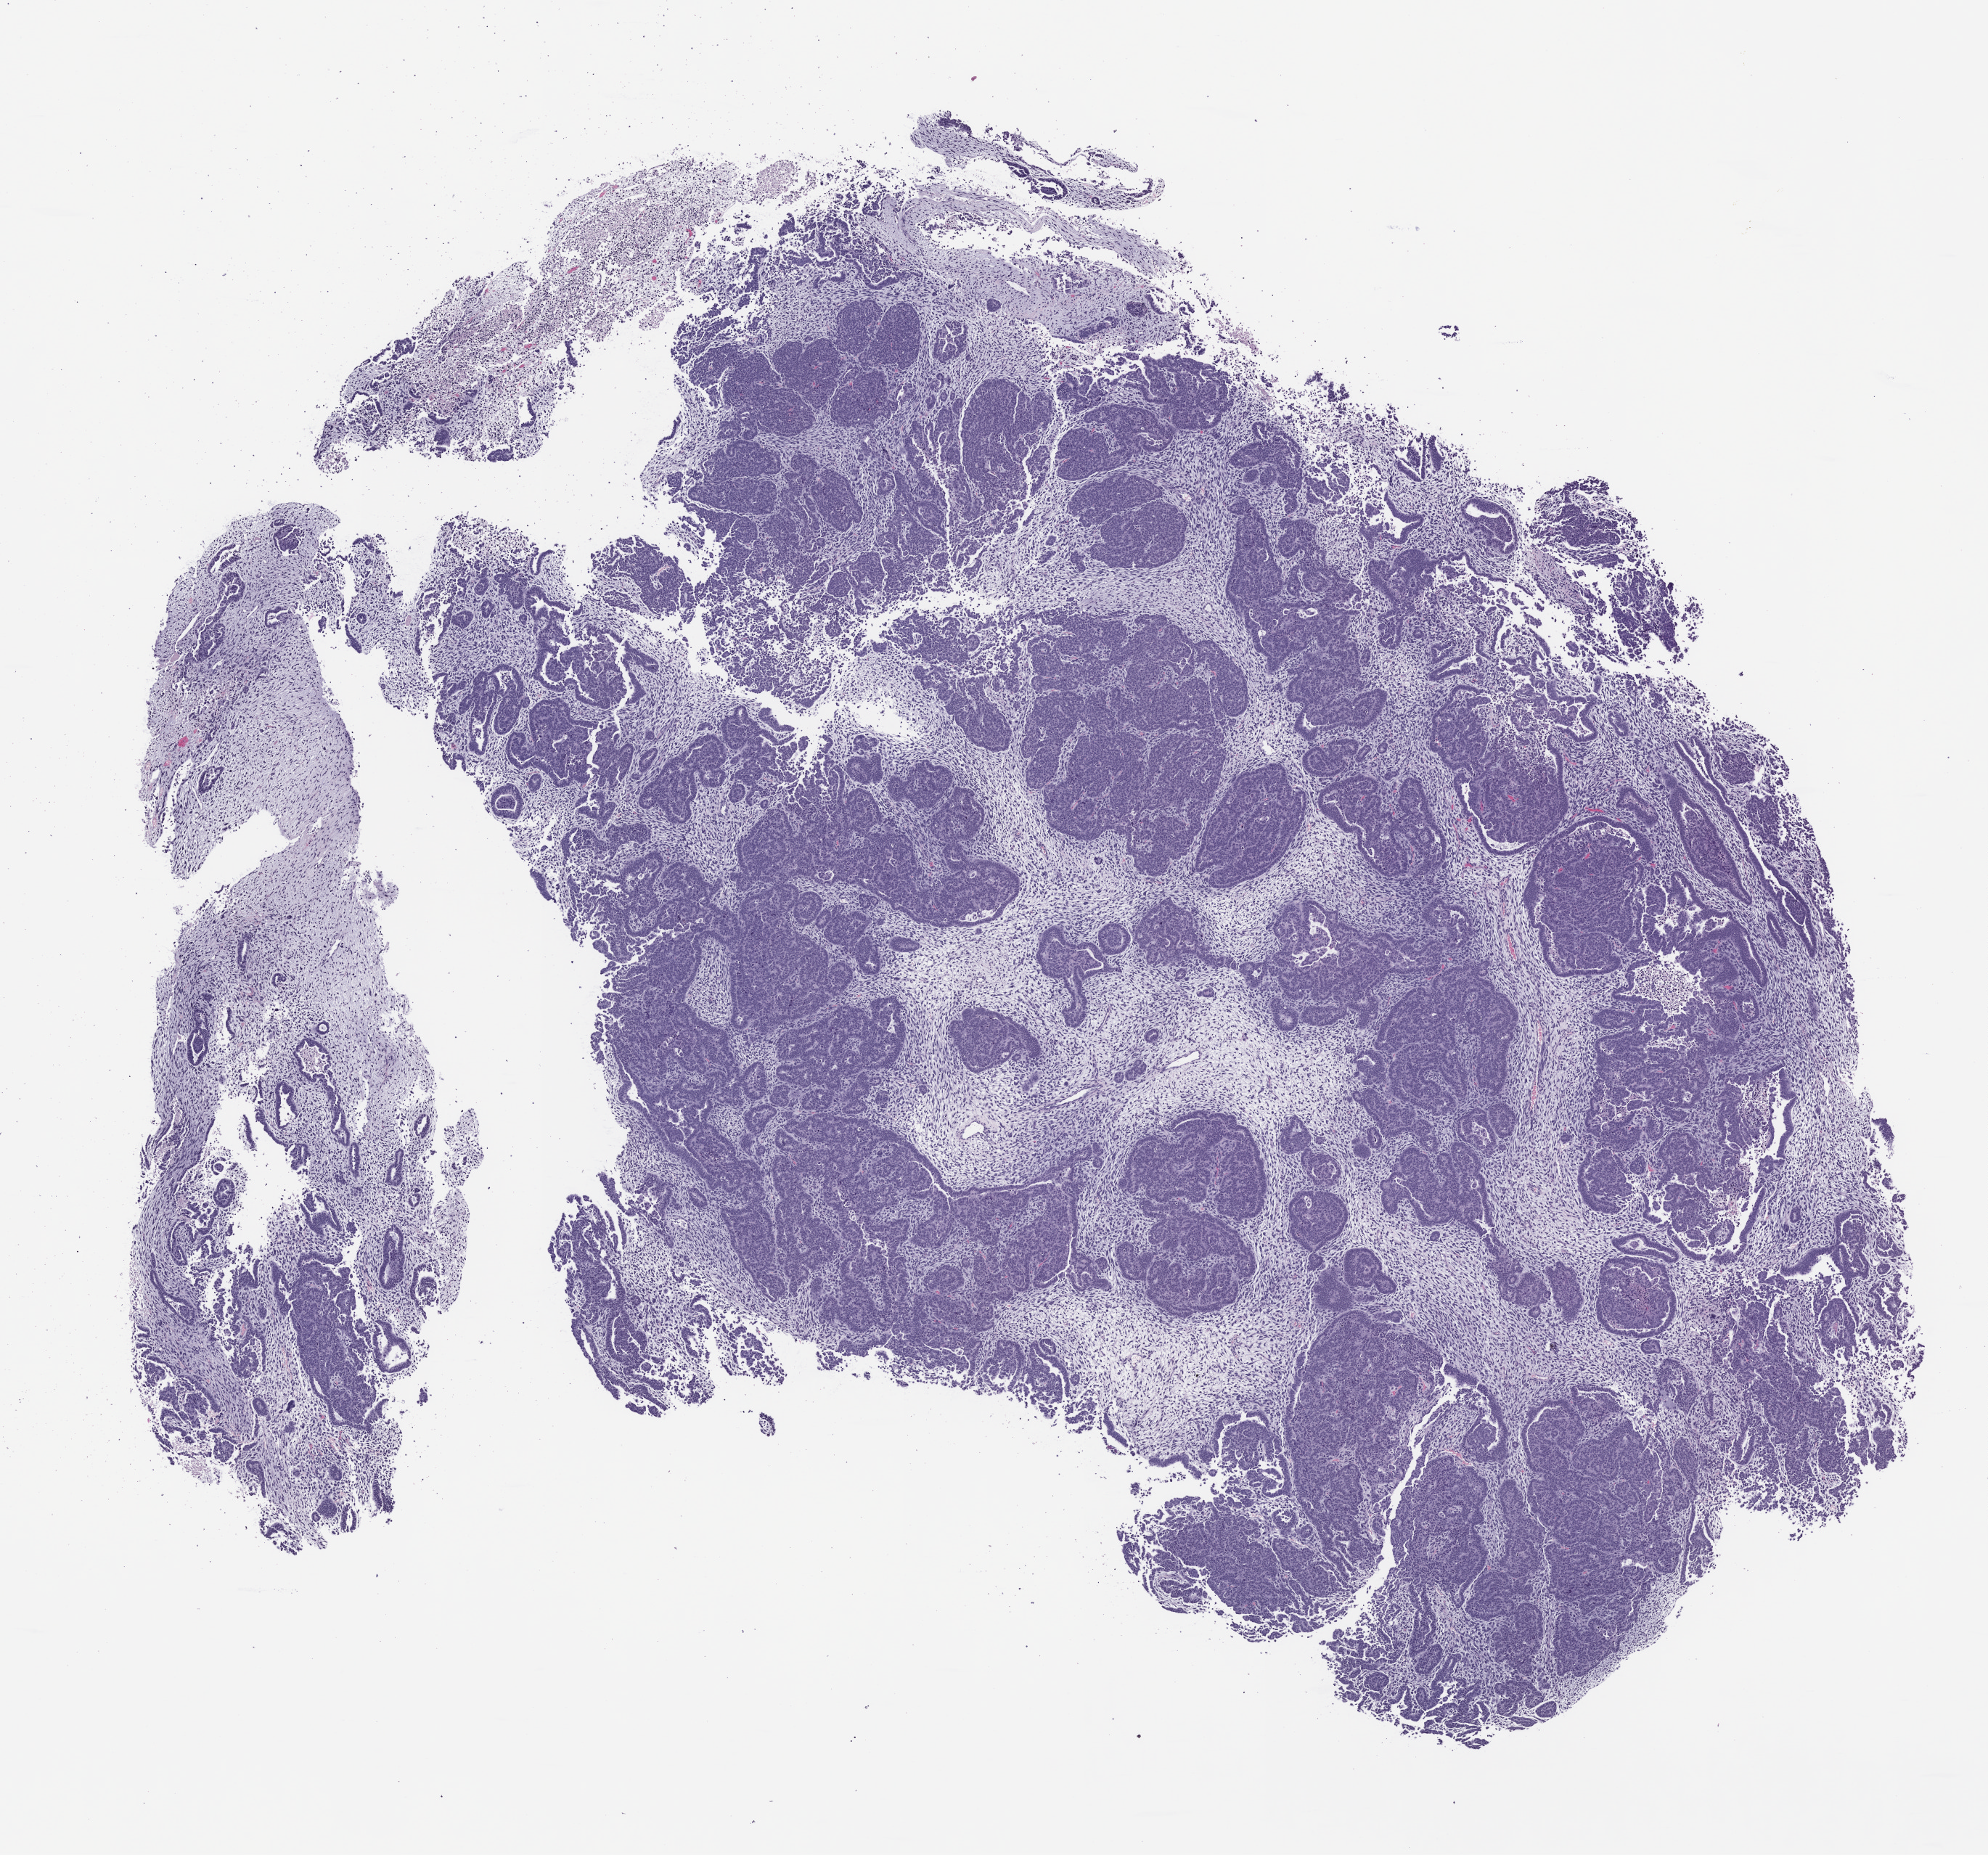
Whole-slide image, H&E: patient-derived xenograft (human tumor grown in a mouse), passage 2 — shown as a low-resolution overview of the whole scanned area (about 11.0 x 10.3 mm), FFPE section, tumor site category: uterus.
- originating patient diagnosis: Carcinosarcoma